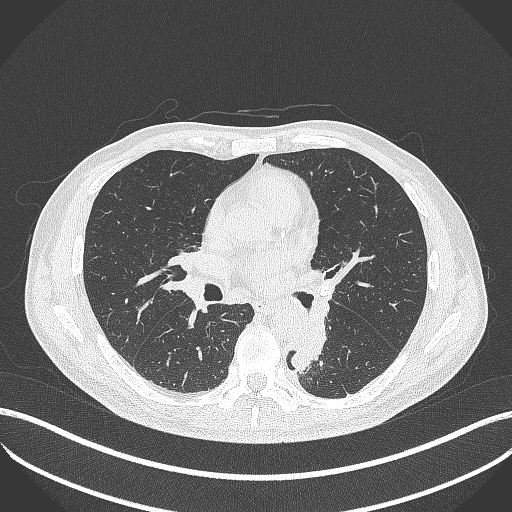
Chest CT, one axial slice. Position 218 of 451 along the scan axis. Lung window (W 1500 / L -600 HU). 1 mm slice thickness. 512 × 512 image matrix, field of view 400 × 400 mm. Patient: male, 72 years. From the clinical record (not read from this slice): clinical TNM (as recorded): T2b N0 M1.
Structures marked on this image (bounding box drawn by a radiologist):
- lung tumour (recorded histology: adenocarcinoma): bounding box (x1, y1, x2, y2) in pixels: (289, 322, 329, 372)